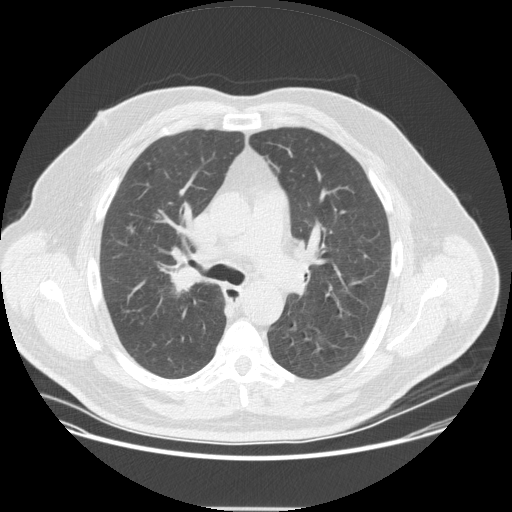
Low-dose screening chest CT, one axial slice. Position 227 of 351 along the scan axis. Reconstruction kernel STANDARD. 120 kVp. Lung window (W 1500 / L -600 HU). 2.5 mm slice thickness. 512 × 512 image matrix.
Structures marked on this image (expert manual segmentation):
- lesion 1 (tumor, upper lobe of right lung): box from (x=167, y=269) to (x=203, y=298) px